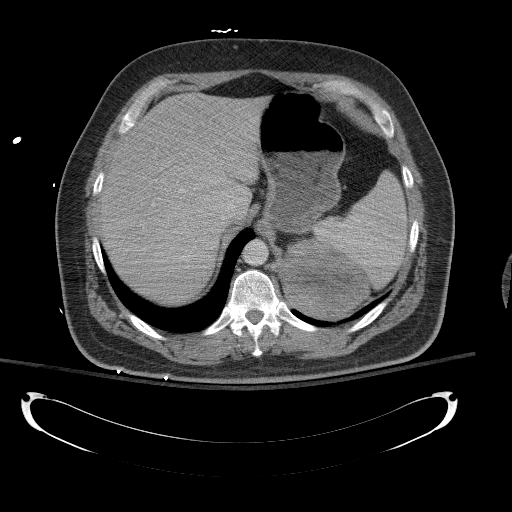
Contrast-enhanced abdominal CT, one axial slice; position 96 of 154 along the scan axis; reconstruction kernel B41f; 120 kVp; intravenous contrast given; soft-tissue window (W 400 / L 40 HU); 5 mm slice thickness; 512 × 512 image matrix, field of view 467 × 467 mm. Male patient, age 43 years. From the clinical record (not read from this slice): diagnosis: adrenocortical carcinoma; tumour side: left adrenal; tumour size at pathology: 9.8 cm; Ki-67 index: 30 %; stage (as recorded): 2.
Annotated regions visible in this slice (semi-automatically segmented with operator editing):
- mass: bounding box <282,240,368,317> (left, top, right, bottom; pixels)